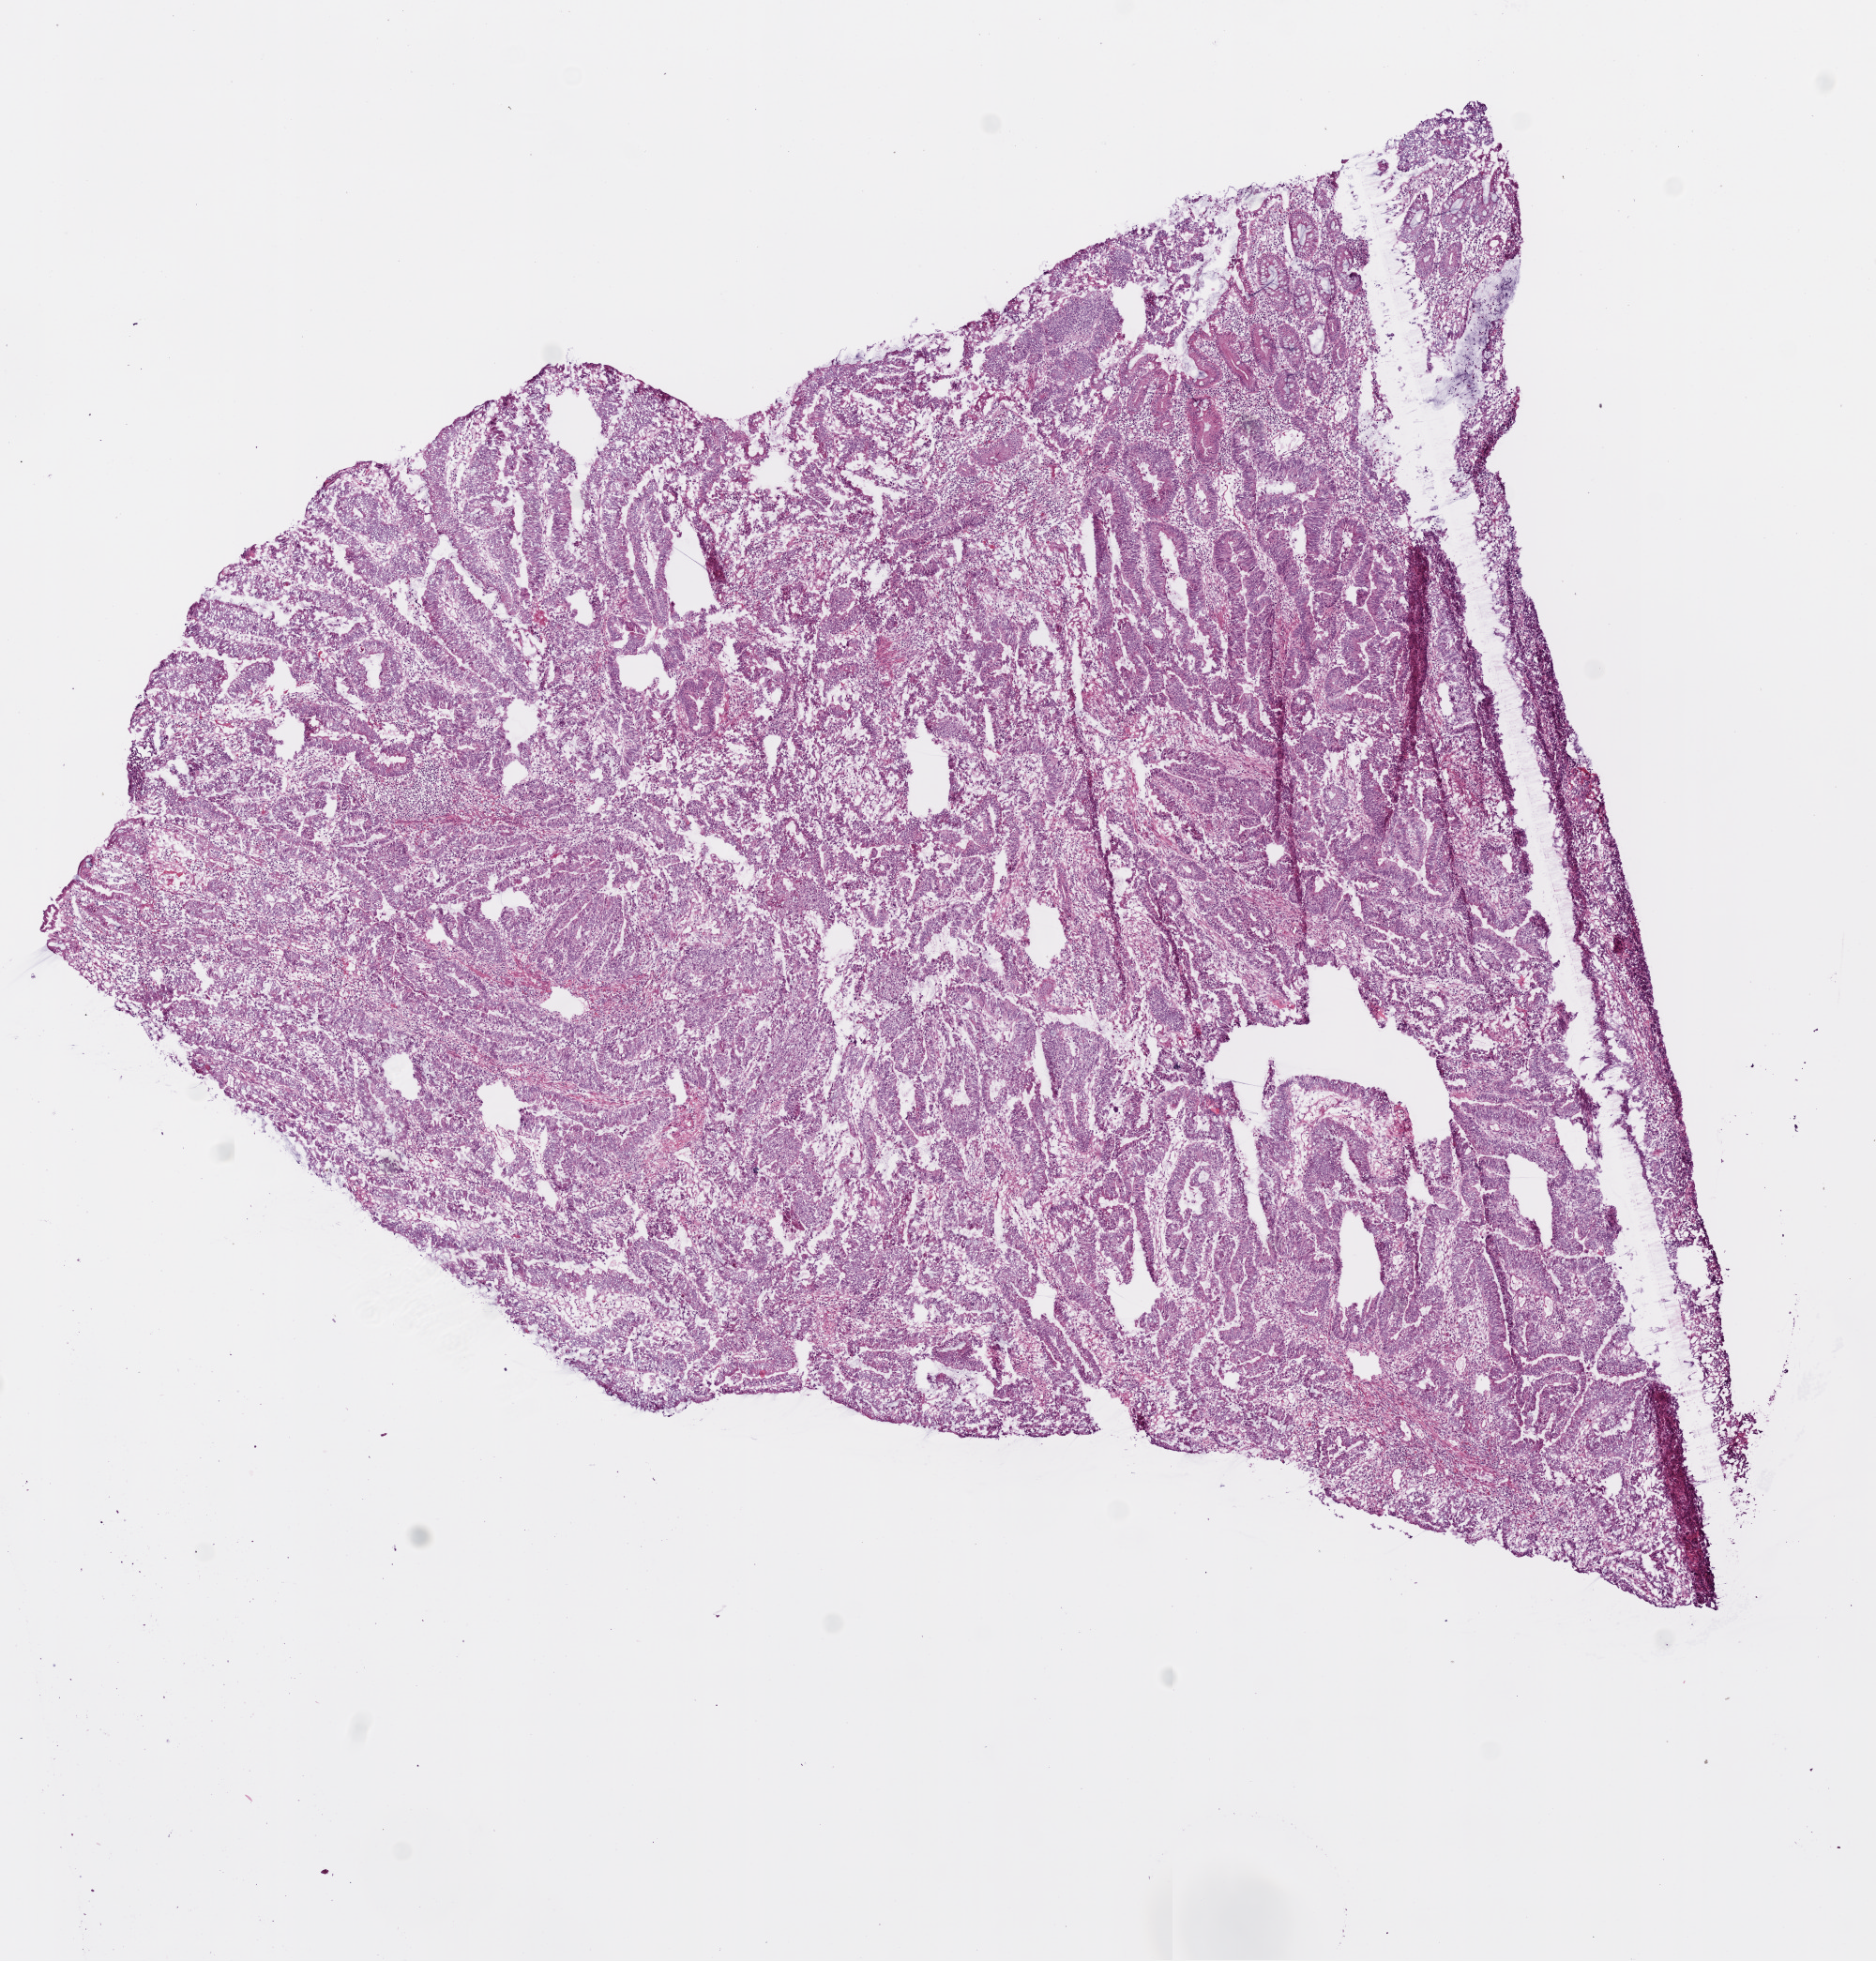
H&E-stained whole-slide image — low-resolution overview of the scanned area, about 8.0 x 8.4 mm, frozen section from the bottom of the tissue portion, sample: primary tumour, colon. Male patient; age at initial diagnosis 74 years. Pathologist review of this section (percent, as recorded): tumour cells 90%, tumour nuclei 85%, normal cells 0%, stromal cells 10%, necrosis 0%.
Lymph nodes positive (case pathology): 0 of 14 examined. AJCC pathologic stage: IIA (6th edition). Diagnosis: Adenocarcinoma, NOS.